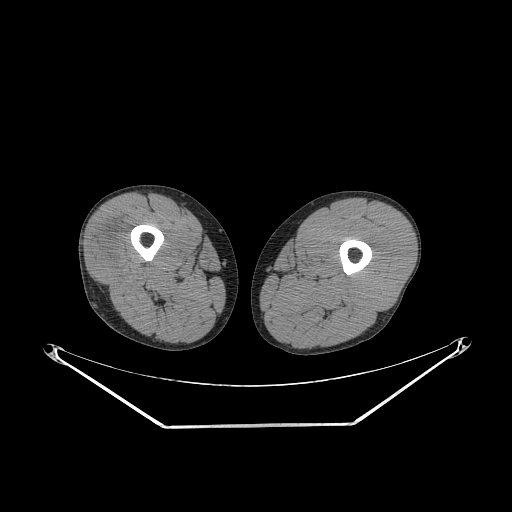
CT of an extremity soft-tissue mass (from a PET/CT study), one axial slice. Reconstruction kernel STANDARD. 140 kVp. Soft-tissue window (W 400 / L 40 HU). 3.75 mm slice thickness. 512 × 512 image matrix. Male patient. From the clinical record (not read from this slice): histological type: poorly differentiated synovial sarcoma; grade: high; site of the primary tumour: right buttock.
Annotated regions visible in this slice (expert contour drawn on MRI and transferred to this co-registered scan by the dataset authors):
- gross tumour volume including surrounding oedema: bounding box [x1, y1, x2, y2] px = [96, 233, 138, 275]